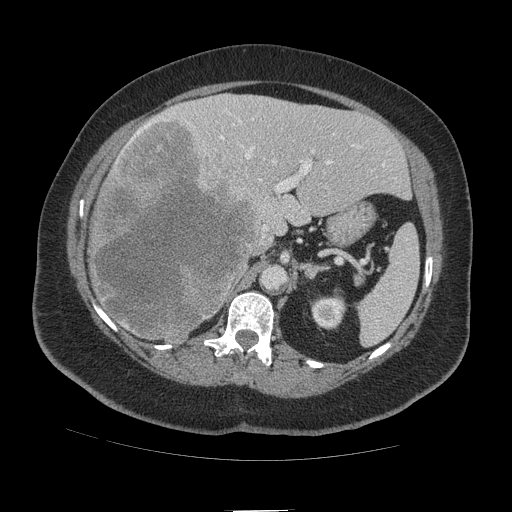
Contrast-enhanced abdominal CT (liver protocol), one axial slice; position 64 of 109 along the scan axis; 140 kVp; soft-tissue window (W 400 / L 40 HU); 2.5 mm slice thickness; 512 × 512 image matrix, field of view 420 × 420 mm. Case-level facts recorded for this patient, not image findings: diagnosis: hepatocellular carcinoma (patient treated with transarterial chemoembolisation; whether this scan precedes or follows treatment is not stated here); TNM stage (as recorded): Stage-IVB; Child-Pugh class: A; tumour differentiation: poorly differentiated; tumour nodularity: multinodular.
Outlined on this slice (semi-automatic segmentation, software-assisted and operator-edited):
- liver parenchyma outside the tumour (the mass and vessels are separate outlines, so this box may not span the whole liver): bounding box <88,94,410,340> (left, top, right, bottom; pixels)
- mass: <89,116,261,344>
- liver vessels: <130,112,385,237>